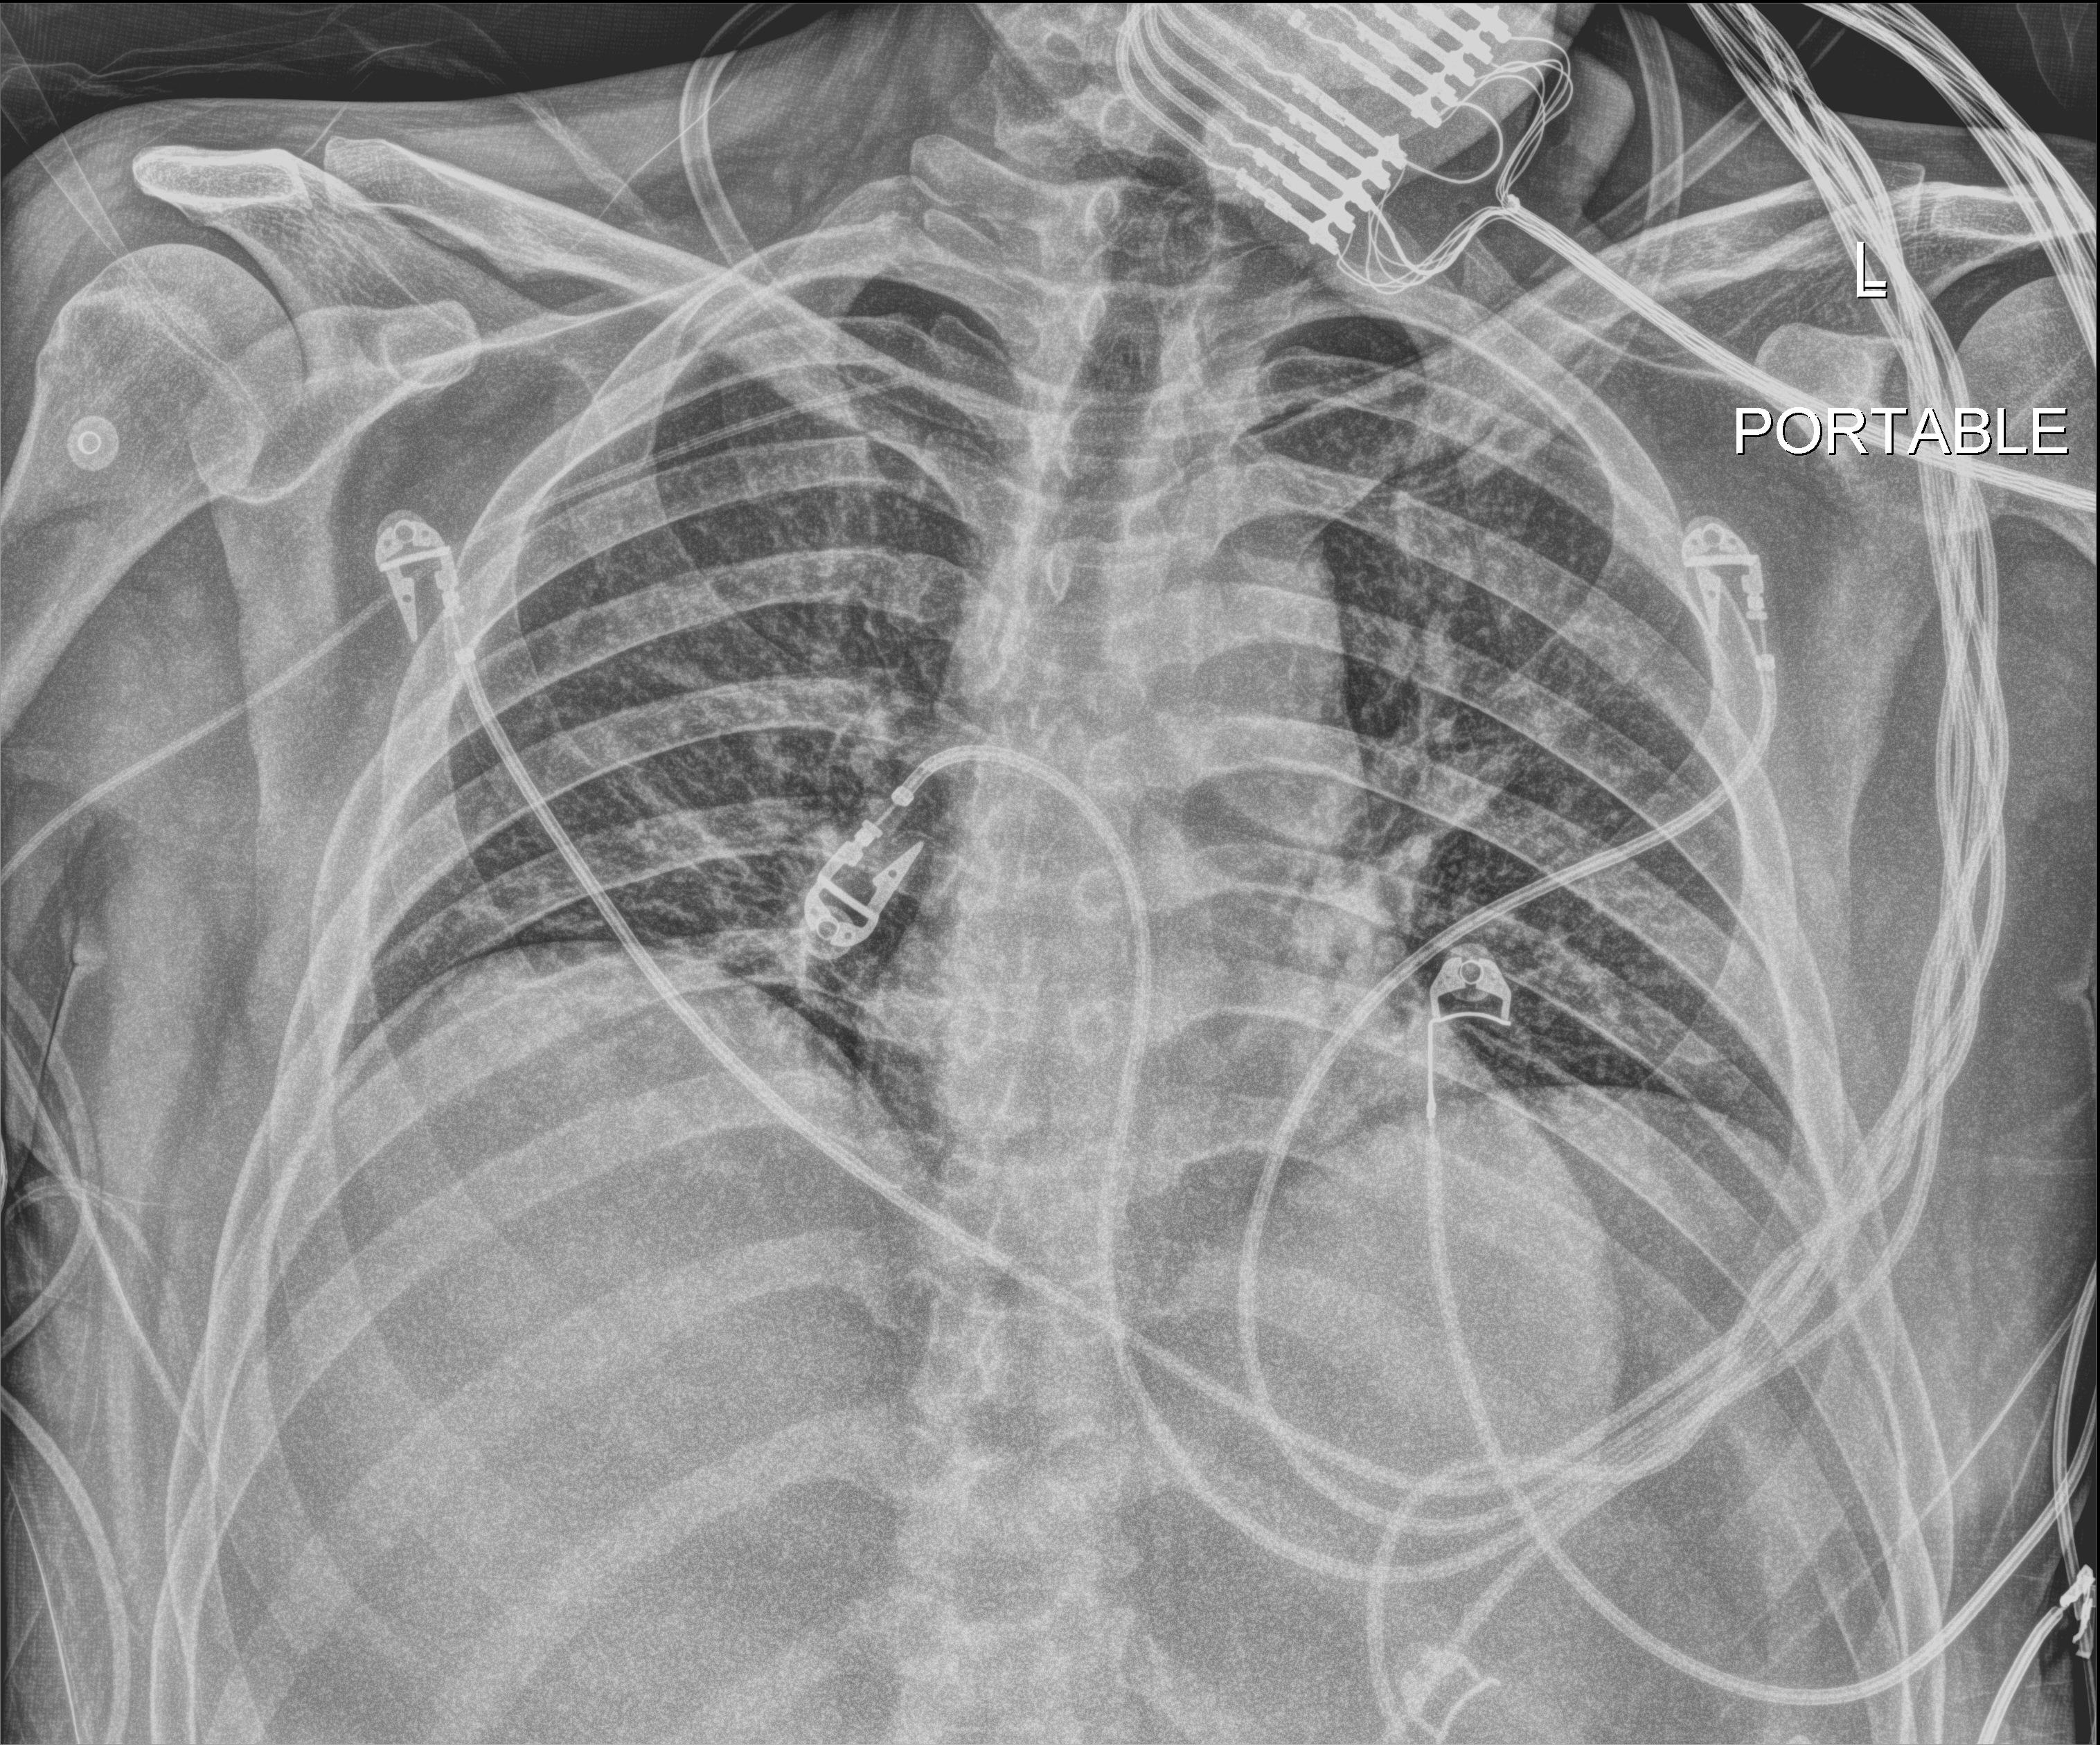
Bedside chest radiograph (digital radiography); anteroposterior (AP) projection. Male patient hospitalised with COVID-19, age 18–59 years.
Admission-level facts for this patient (not findings on this image; timing relative to this image not recorded): mechanically ventilated during this hospital stay: yes.